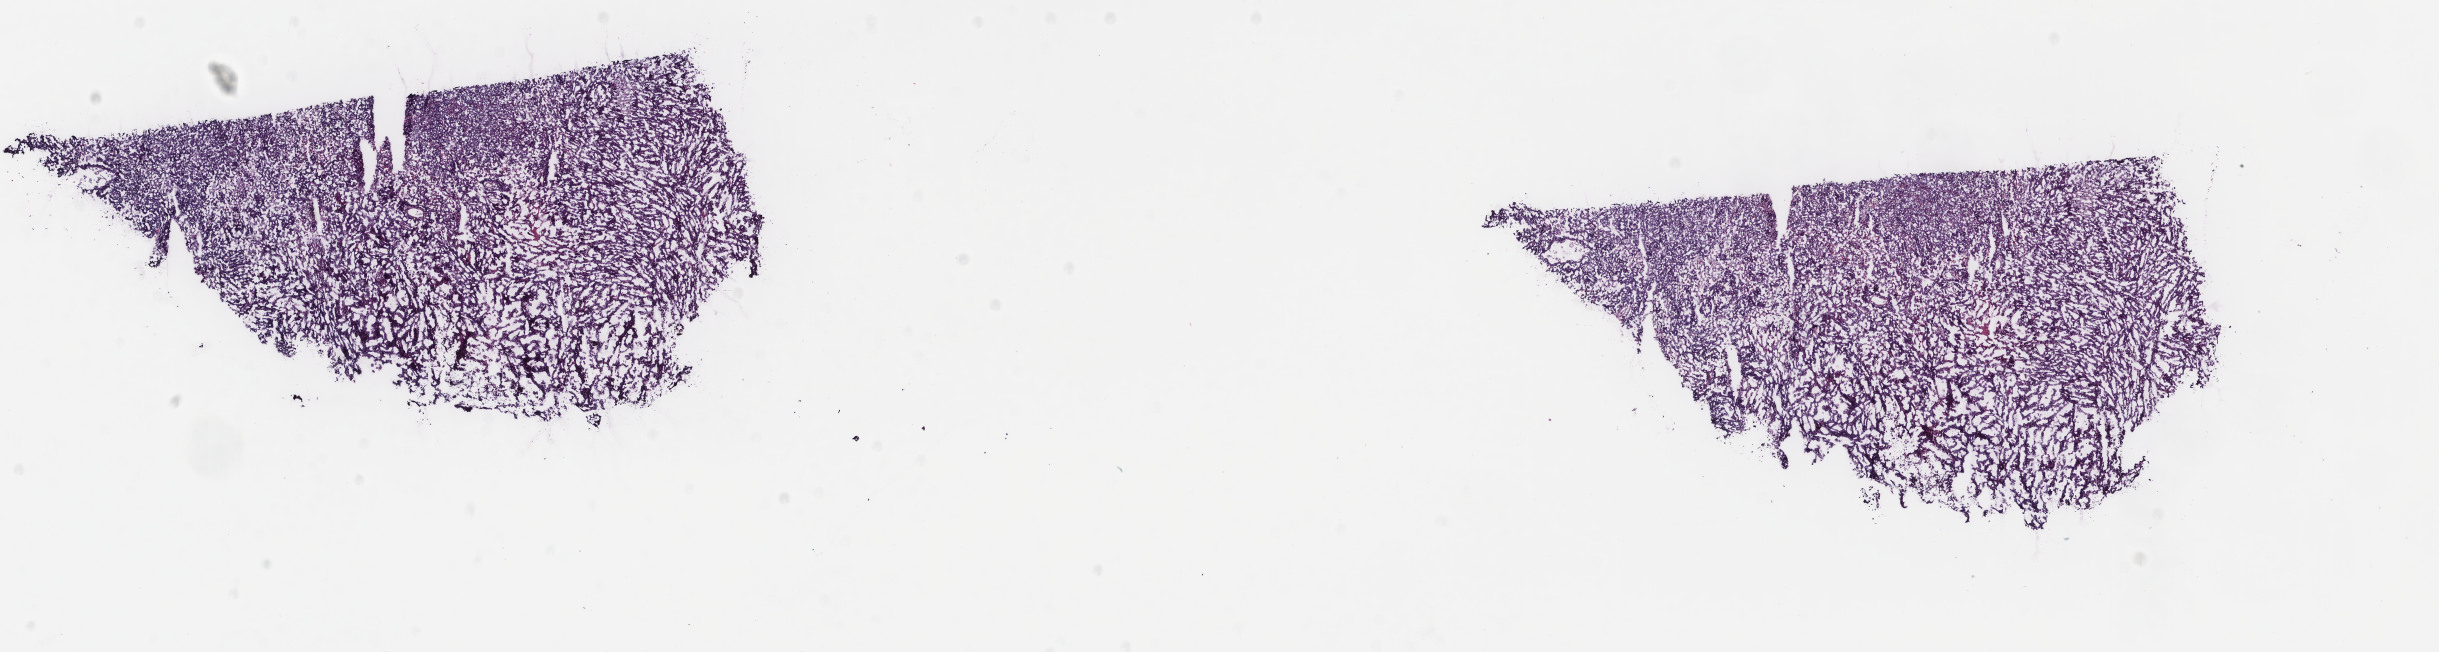
Digitized H&E-stained tissue section (whole slide) — low-resolution overview of the scanned area, about 19.4 x 5.2 mm, frozen section from the top of the tissue portion, uterus, primary tumour sample. Patient: female, age at initial diagnosis 69 years. Histologic grade: high grade. Composition of this section per pathologist review: tumour cells 90%, tumour nuclei 90%, normal cells 0%, stromal cells 5%, necrosis 5%. Inflammatory infiltration, as recorded: lymphocyte infiltration 60%, monocyte infiltration 20%, neutrophil infiltration 10%.
• pathologic diagnosis: Serous cystadenocarcinoma, NOS (endometrium)
• FIGO stage: IV